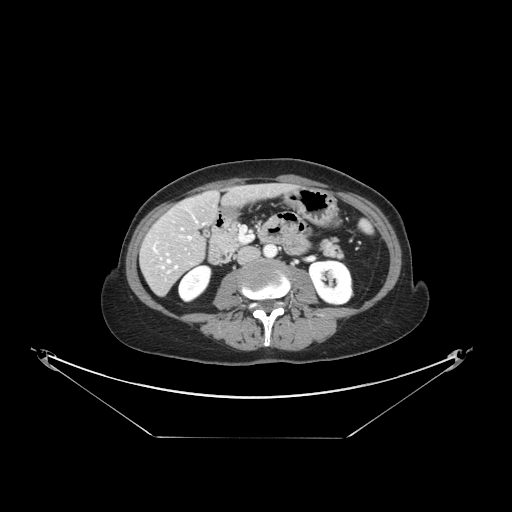
Contrast-enhanced abdominal CT, one axial slice. Slice 49 of 148 in the series (ordered by position). 120 kVp. Intravenous contrast given. Soft-tissue window (W 400 / L 40 HU). 2.5 mm slice thickness. 512 × 512 image matrix, field of view 500 × 500 mm. Female patient, age 73 years. From the clinical record (not read from this slice): diagnosis: colorectal cancer liver metastases, imaged before liver resection; multiple liver metastases: no; largest metastasis: 1 cm; disease in both lobes: no.
Annotated regions visible in this slice (outlined manually by an expert reader):
- hepatic veins: bounding box (x1, y1, x2, y2) in pixels: (153, 220, 198, 269)
- liver: (143, 185, 288, 294)
- planned liver remnant (the part of the liver to remain after resection): (162, 185, 288, 246)